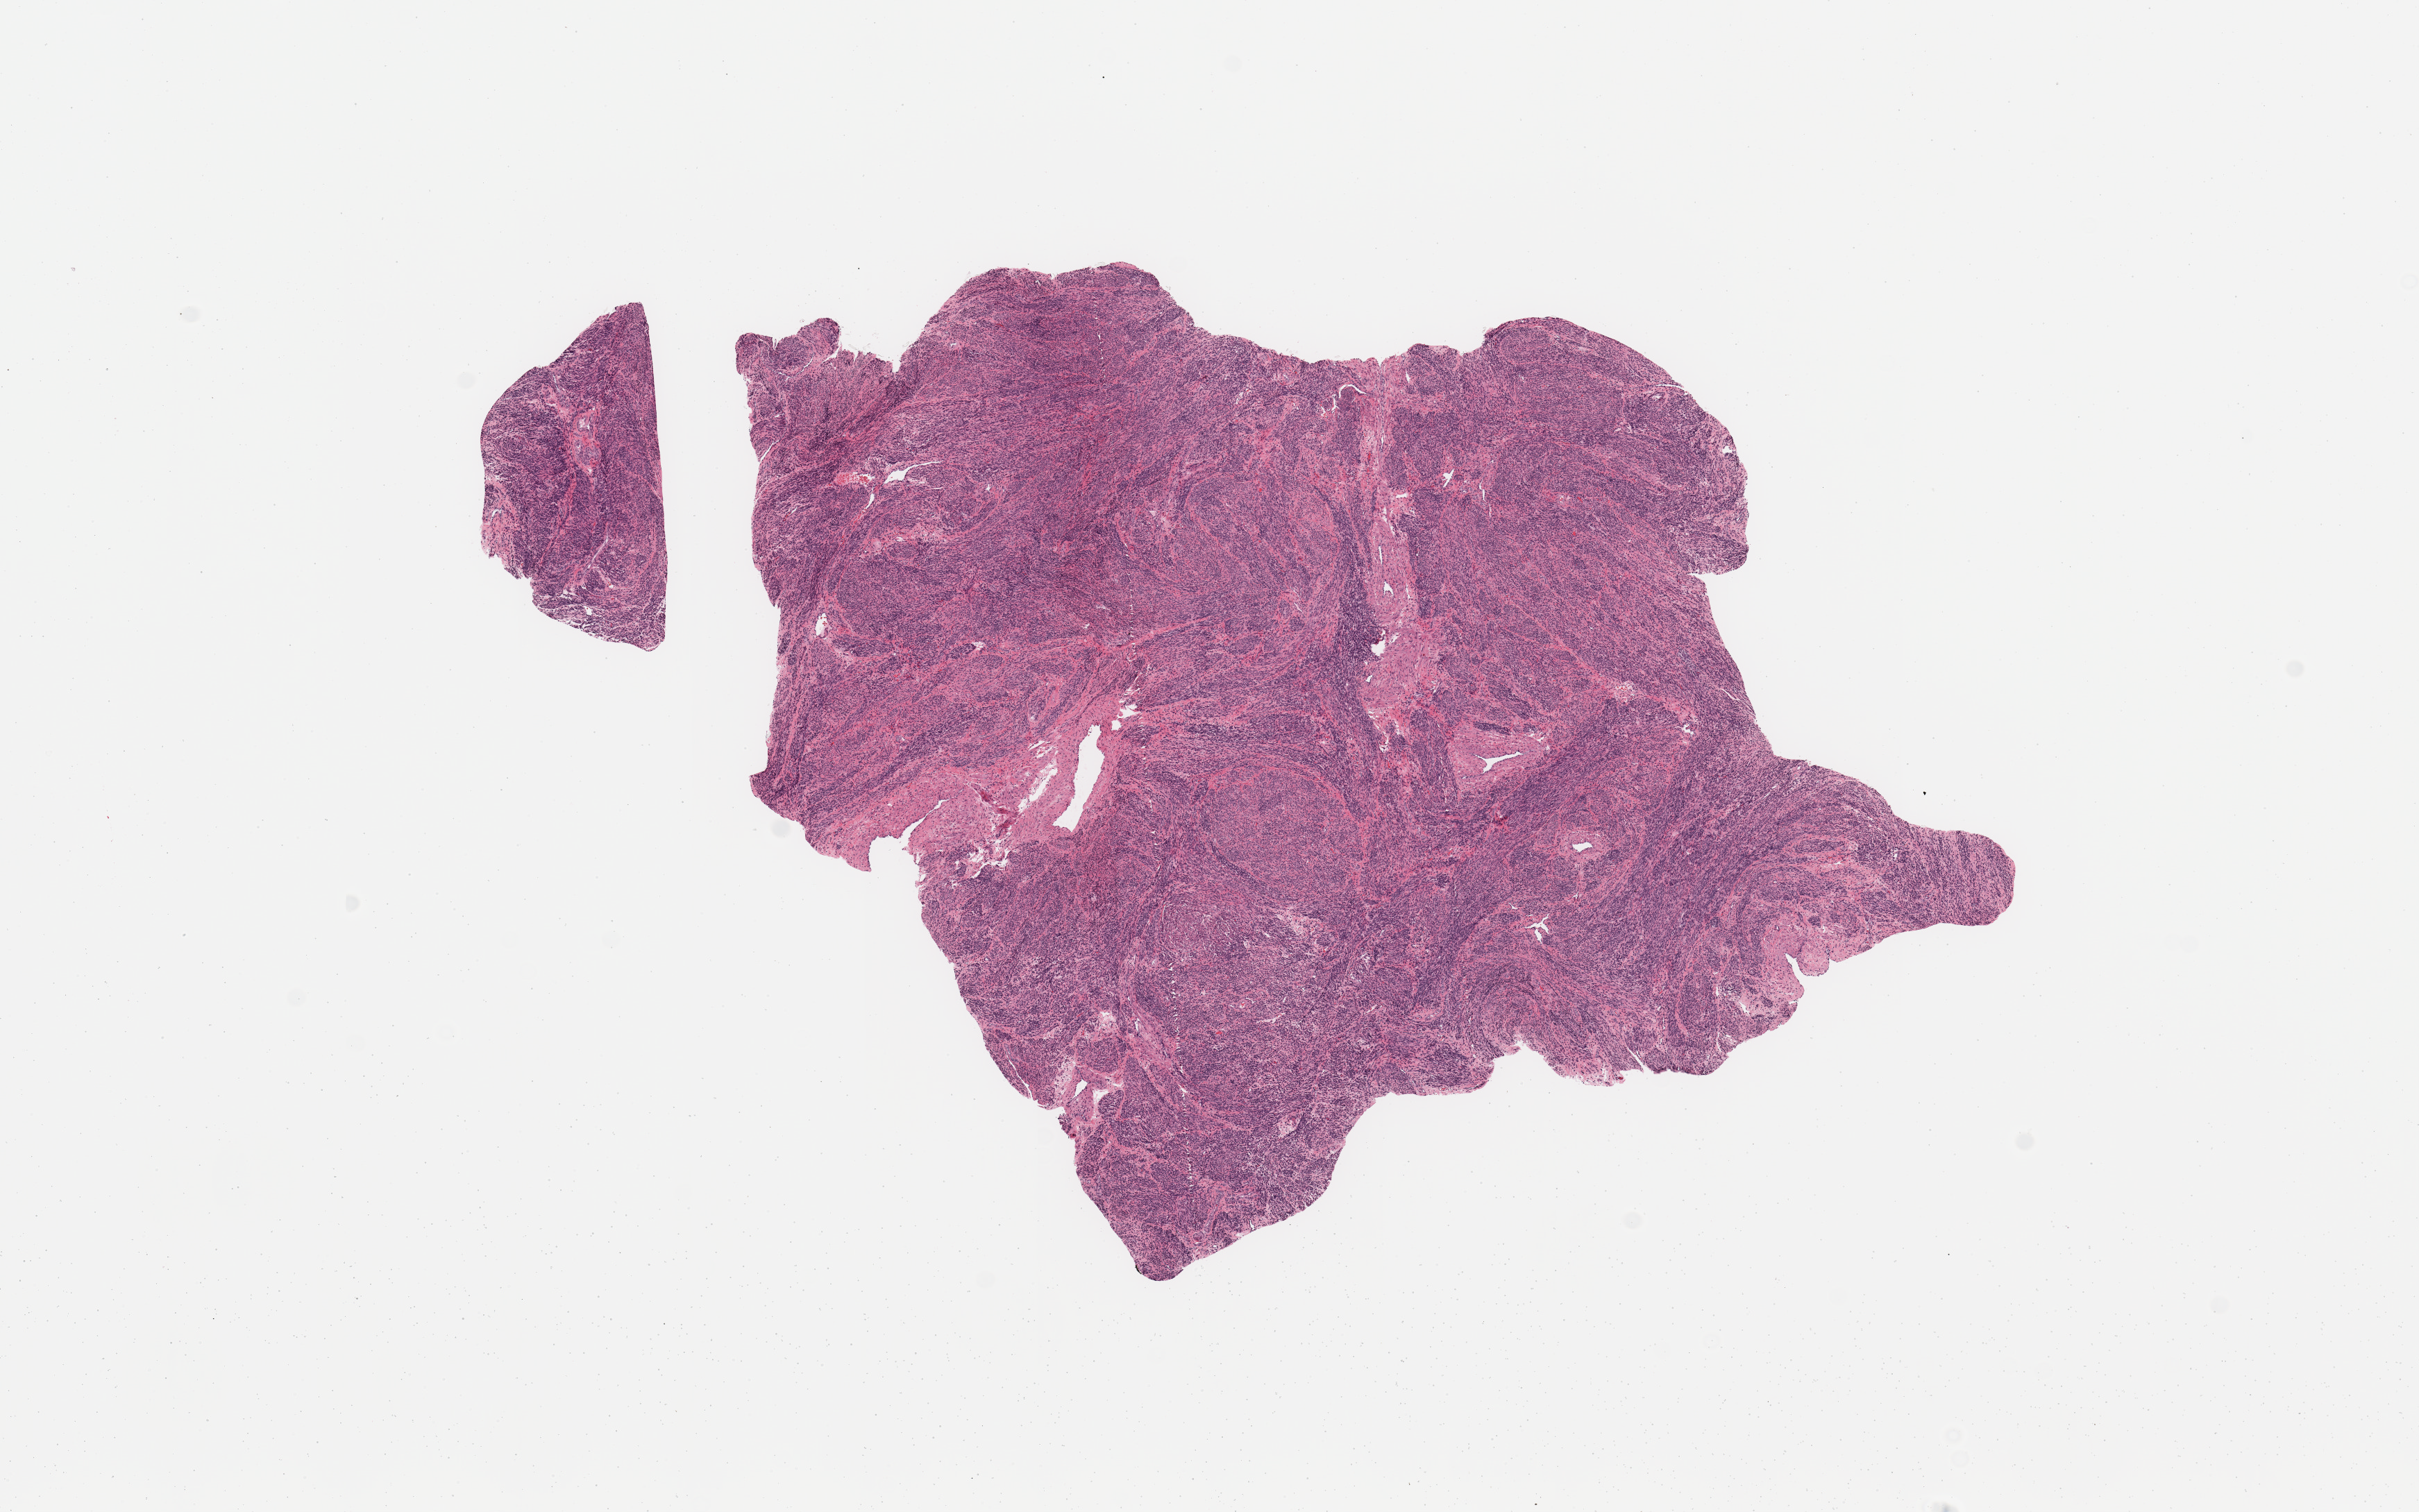
Digitized H&E-stained tissue section (whole slide) — low-resolution overview of the scanned area, about 13.8 x 8.6 mm; normal (non-tumour) tissue sample, sampled site: uterus. Patient: female, age 54 years.
- this section: normal (non-tumour) tissue from the same patient
- patient diagnosis: Endometrioid adenocarcinoma, NOS